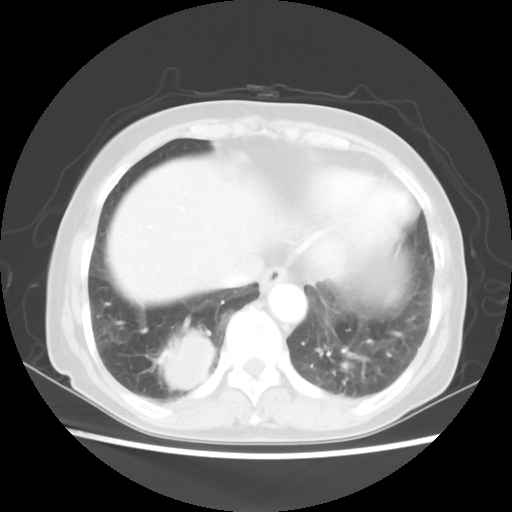
Chest CT, one axial slice; position 17 of 56 along the scan axis; lung window (W 1500 / L -600 HU); 512 × 512 image matrix, field of view 332 × 332 mm. Patient: female, 66 years. From the clinical record (not read from this slice): clinical TNM (as recorded): T2 N3 M0; histopathological grade: G3.
Annotated regions visible in this slice (rectangle marked by the reading radiologist):
- lung tumour (recorded histology: small cell carcinoma): bounding box [x1, y1, x2, y2] px = [151, 327, 220, 396]